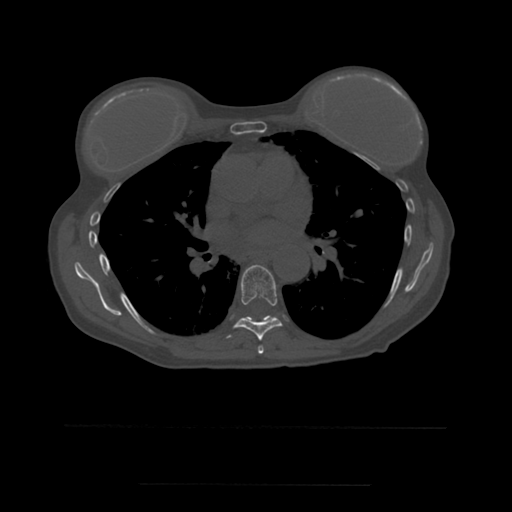
CT including the spine, one axial slice; bone window (W 1800 / L 400 HU); 512 × 512 image matrix, field of view 350 × 350 mm. Patient age 58 years. From the clinical record (not read from this slice): primary cancer: lung.
Structures marked on this image (semi-automatically segmented with operator editing):
- T6 vertebra: bounding box [x1, y1, x2, y2] px = [258, 346, 264, 354]
- T7 vertebra: [227, 265, 283, 341]
- T8 vertebra: [262, 317, 265, 322]